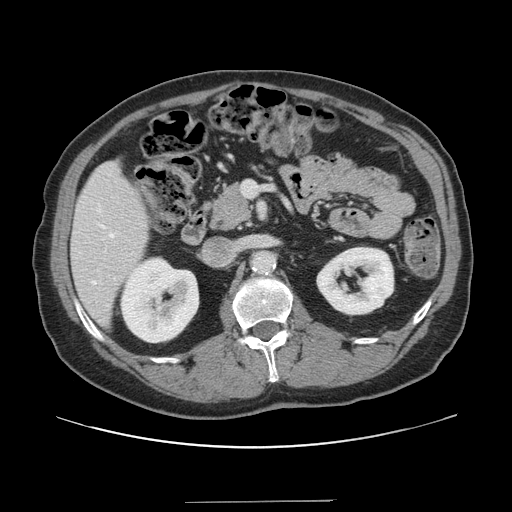
Contrast-enhanced abdominal CT, one axial slice; position 67 of 151 along the scan axis; intravenous contrast given; soft-tissue window (W 400 / L 40 HU); 2.5 mm slice thickness; 512 × 512 image matrix, field of view 399 × 399 mm. Male patient, age 63 years. Case-level facts recorded for this patient, not image findings: diagnosis: colorectal cancer liver metastases, imaged before liver resection; multiple liver metastases: no; largest metastasis: 2.1 cm; disease in both lobes: no.
Outlined on this slice (outlined manually by an expert reader):
- hepatic veins: box from (x=92, y=210) to (x=114, y=284) px
- liver: (x=73, y=162)–(x=149, y=325)
- planned liver remnant (the part of the liver to remain after resection): (x=72, y=162)–(x=149, y=326)
- portal vein (with intrahepatic branches): (x=104, y=181)–(x=258, y=252)